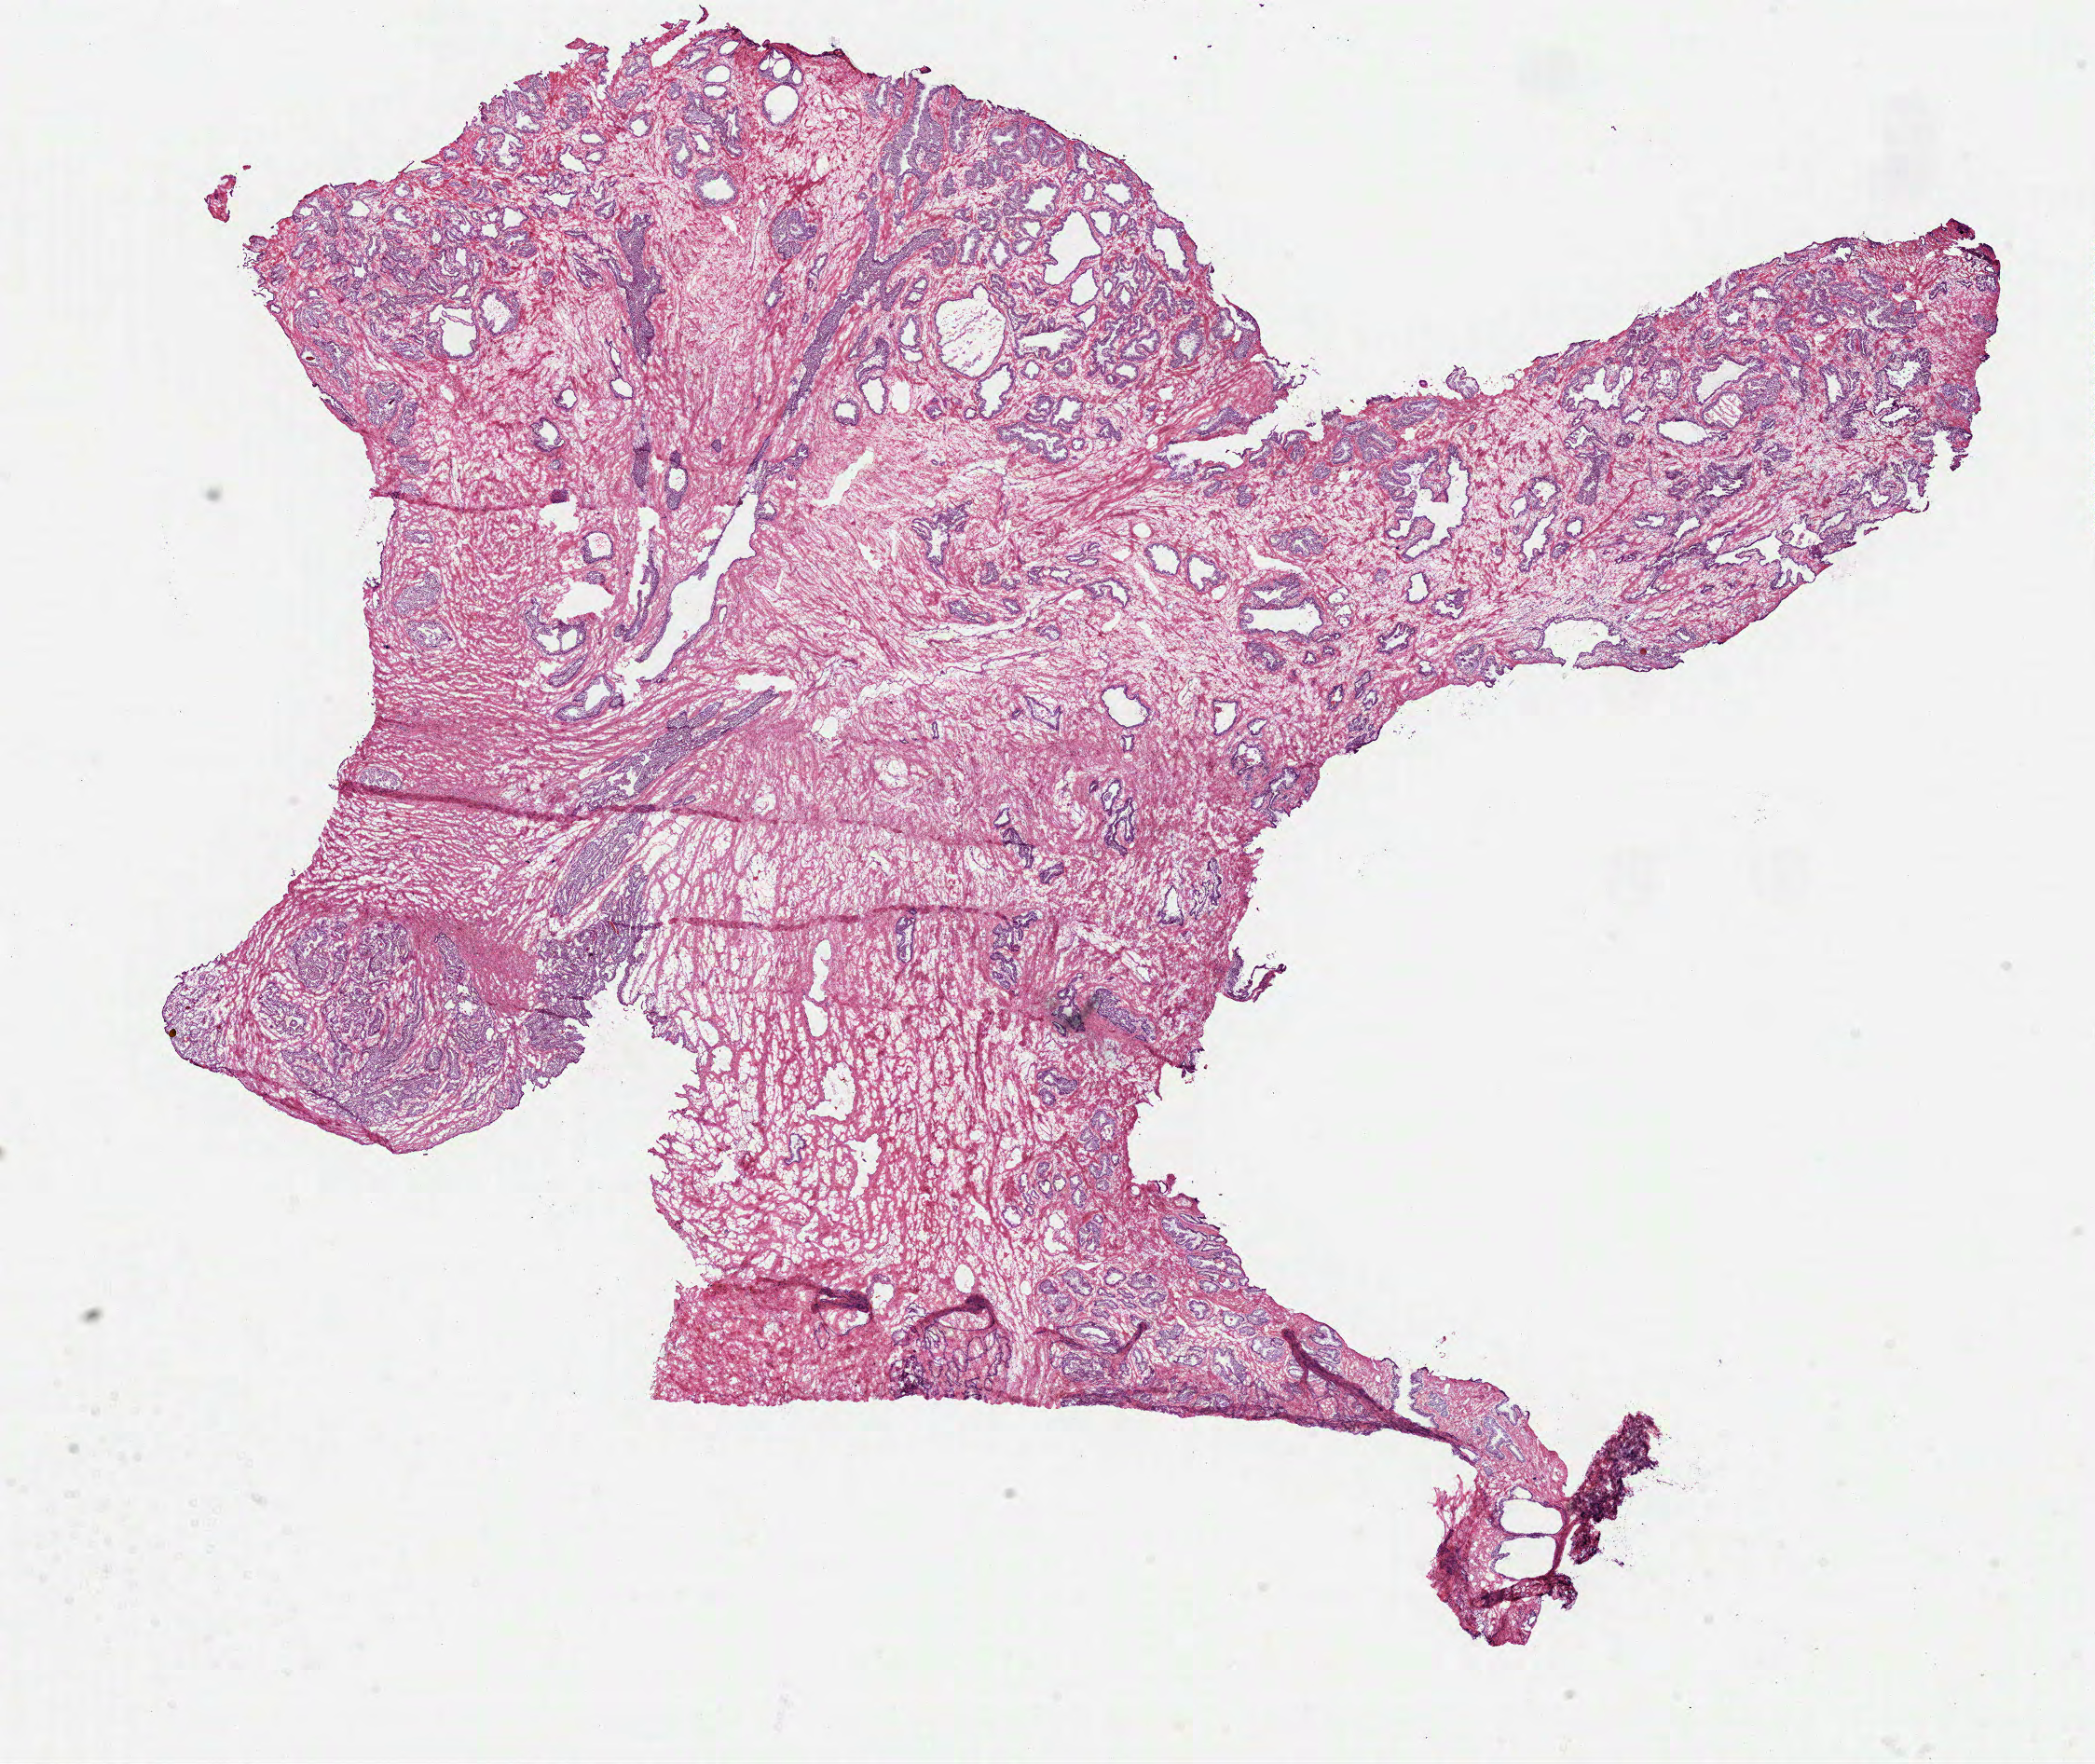
Whole-slide histology image, H&E-stained — shown as a low-resolution overview of the whole scanned area (about 18.1 x 15.3 mm, slide scanned at 40x). Frozen section from the top of the tissue portion. Sample: solid tissue normal (non-tumour tissue), prostate. Patient: male, age at initial diagnosis 63 years.
This section: solid tissue normal sample (biorepository sample class). Patient diagnosis: Acinar cell carcinoma.